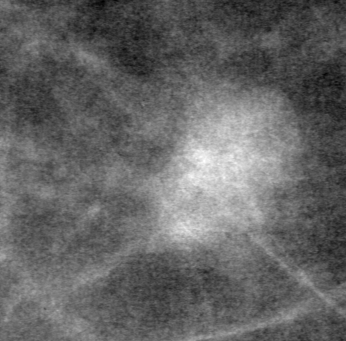
Crop from a digitized film mammogram around one marked abnormality; left breast; CC view.
Marked abnormality: mass, shape oval, margins obscured; BI-RADS assessment category 0; subtlety rating 5 on a 1 (subtle) to 5 (obvious) scale; pathology (as recorded): benign.